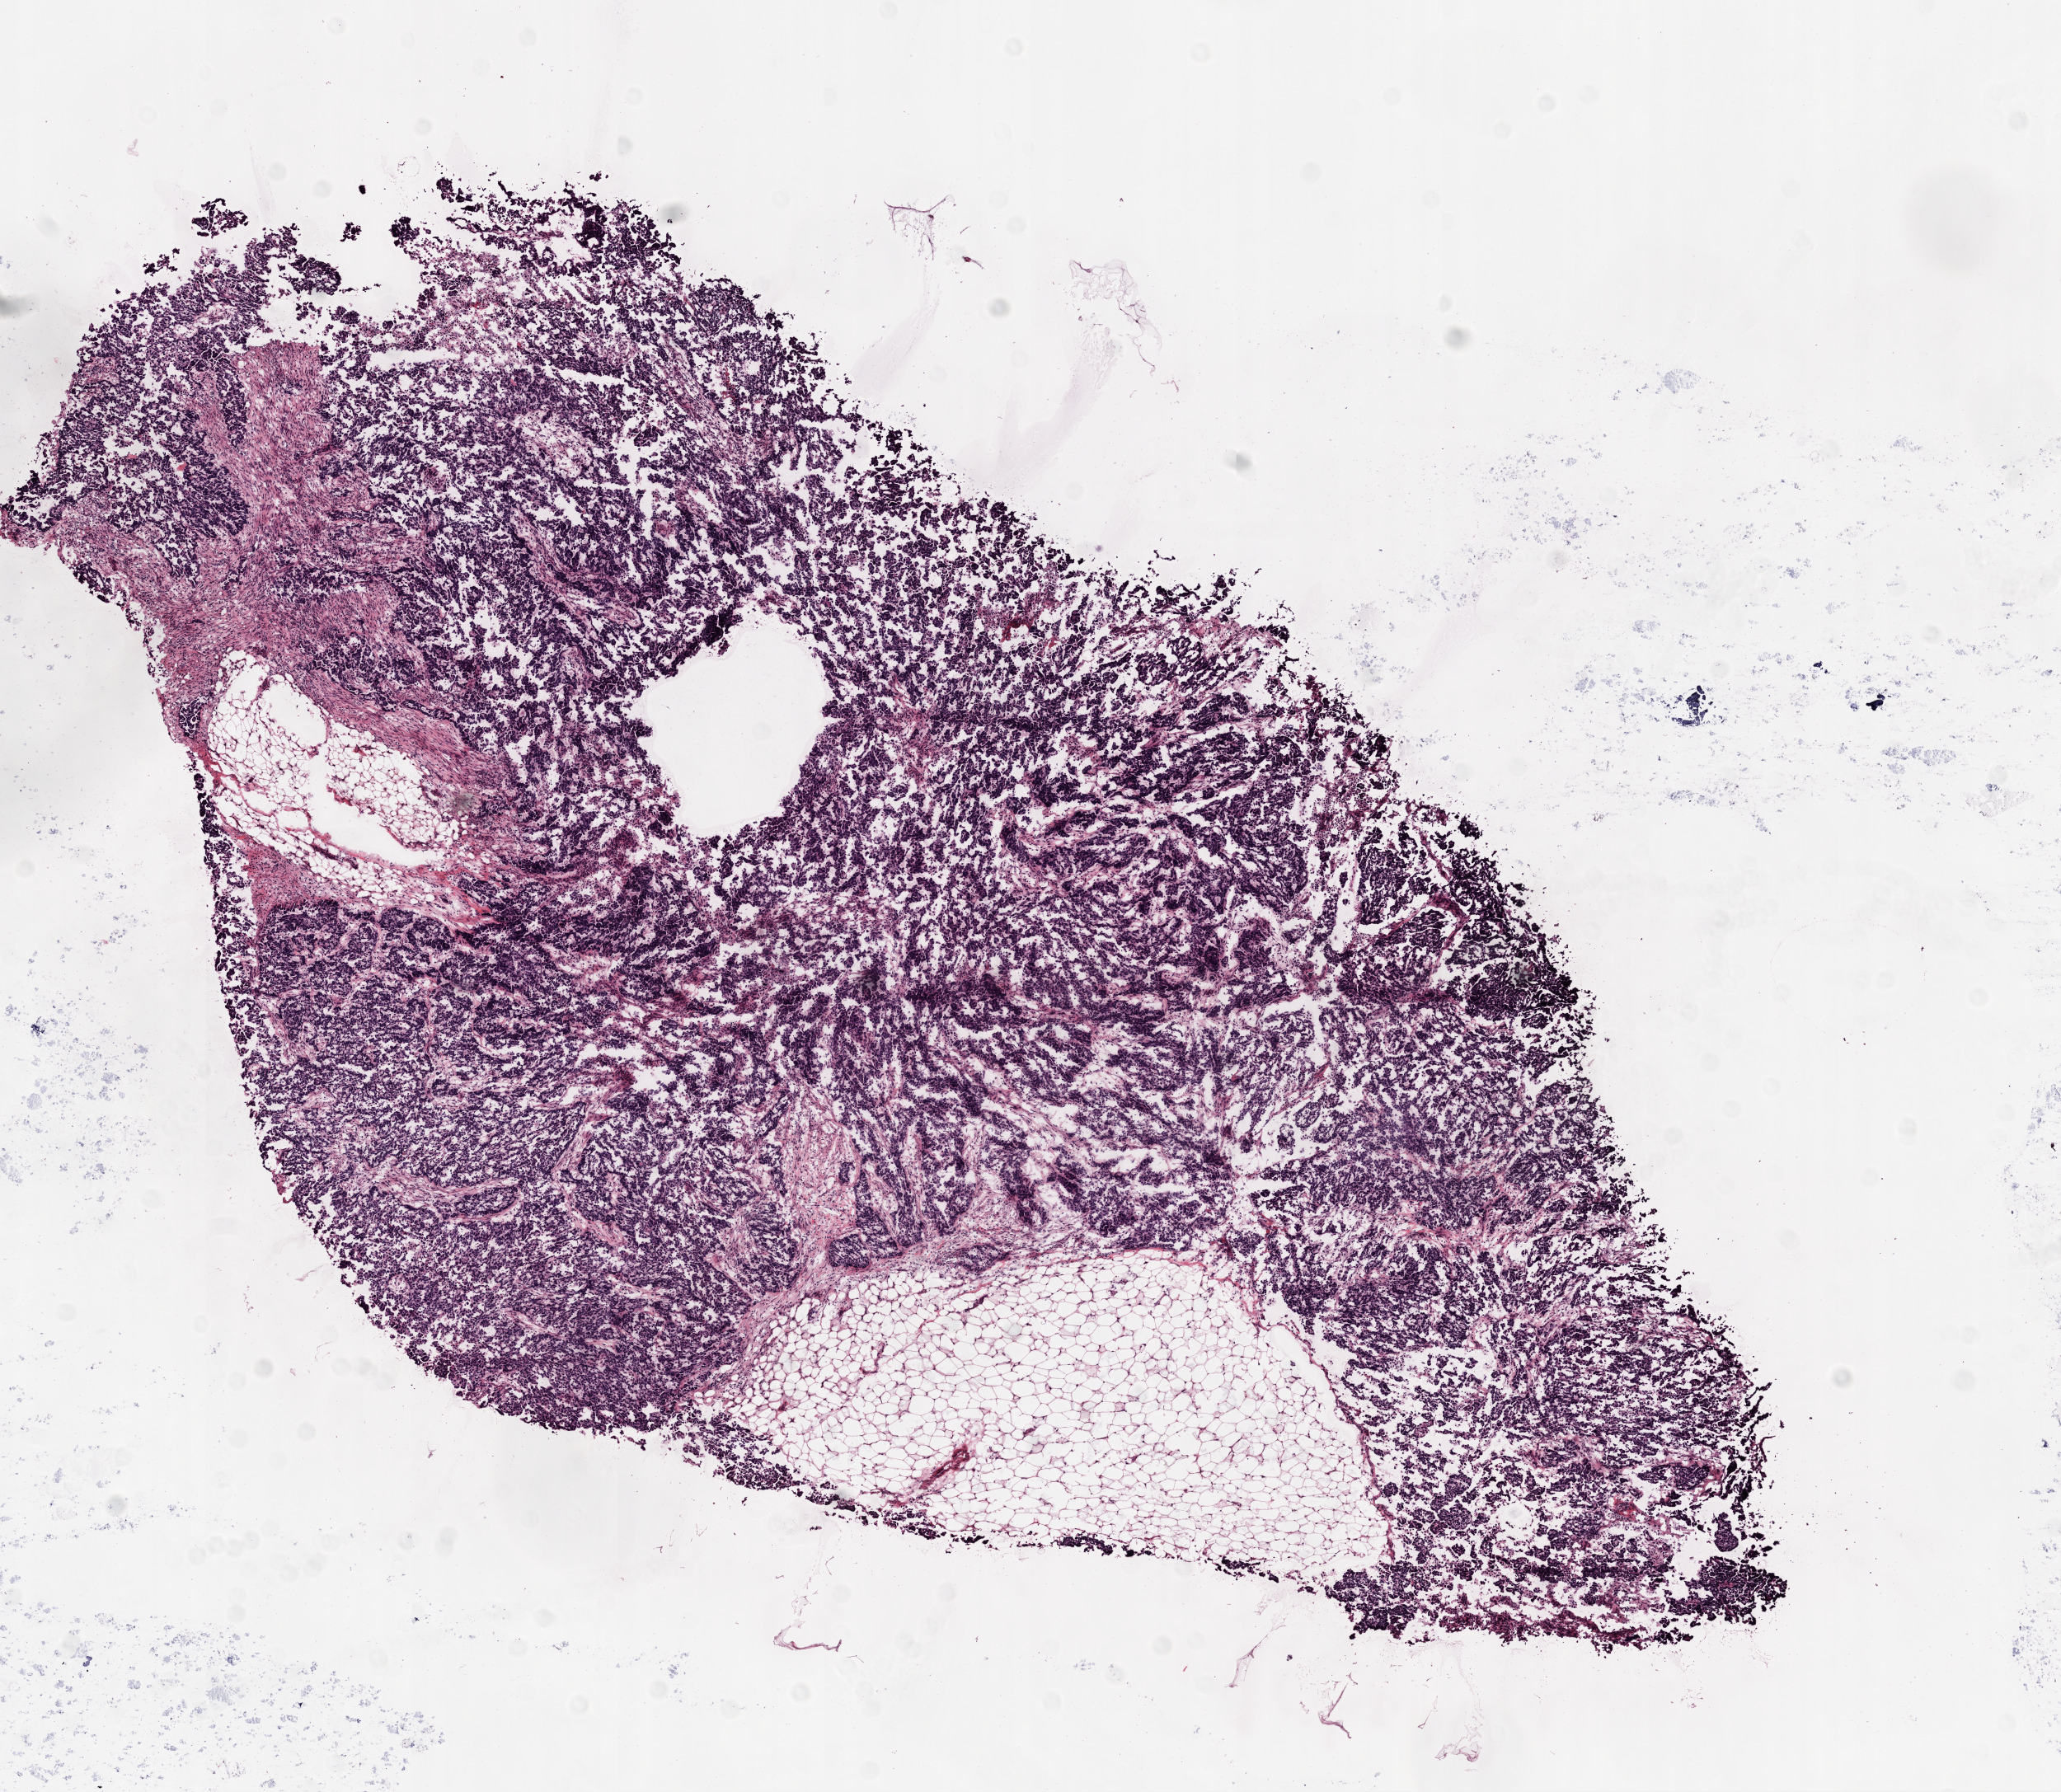
Whole-slide histology image, H&E — a low-resolution overview of the entire scanned area, about 10.0 x 8.7 mm (slide scanned at 20x). Frozen section from the top of the tissue portion. Primary tumour sample from the ovary. Female patient; age at initial diagnosis 40 years. Histologic grade: G3 (poorly differentiated). Slide review estimates, as recorded: tumour cells 85%, tumour nuclei 90%, normal cells 10%, stromal cells 5%, necrosis 0%. Infiltration values recorded for this section: lymphocyte infiltration 2%.
Laterality: bilateral. Diagnosis: Serous cystadenocarcinoma, NOS. FIGO stage: IIIC.